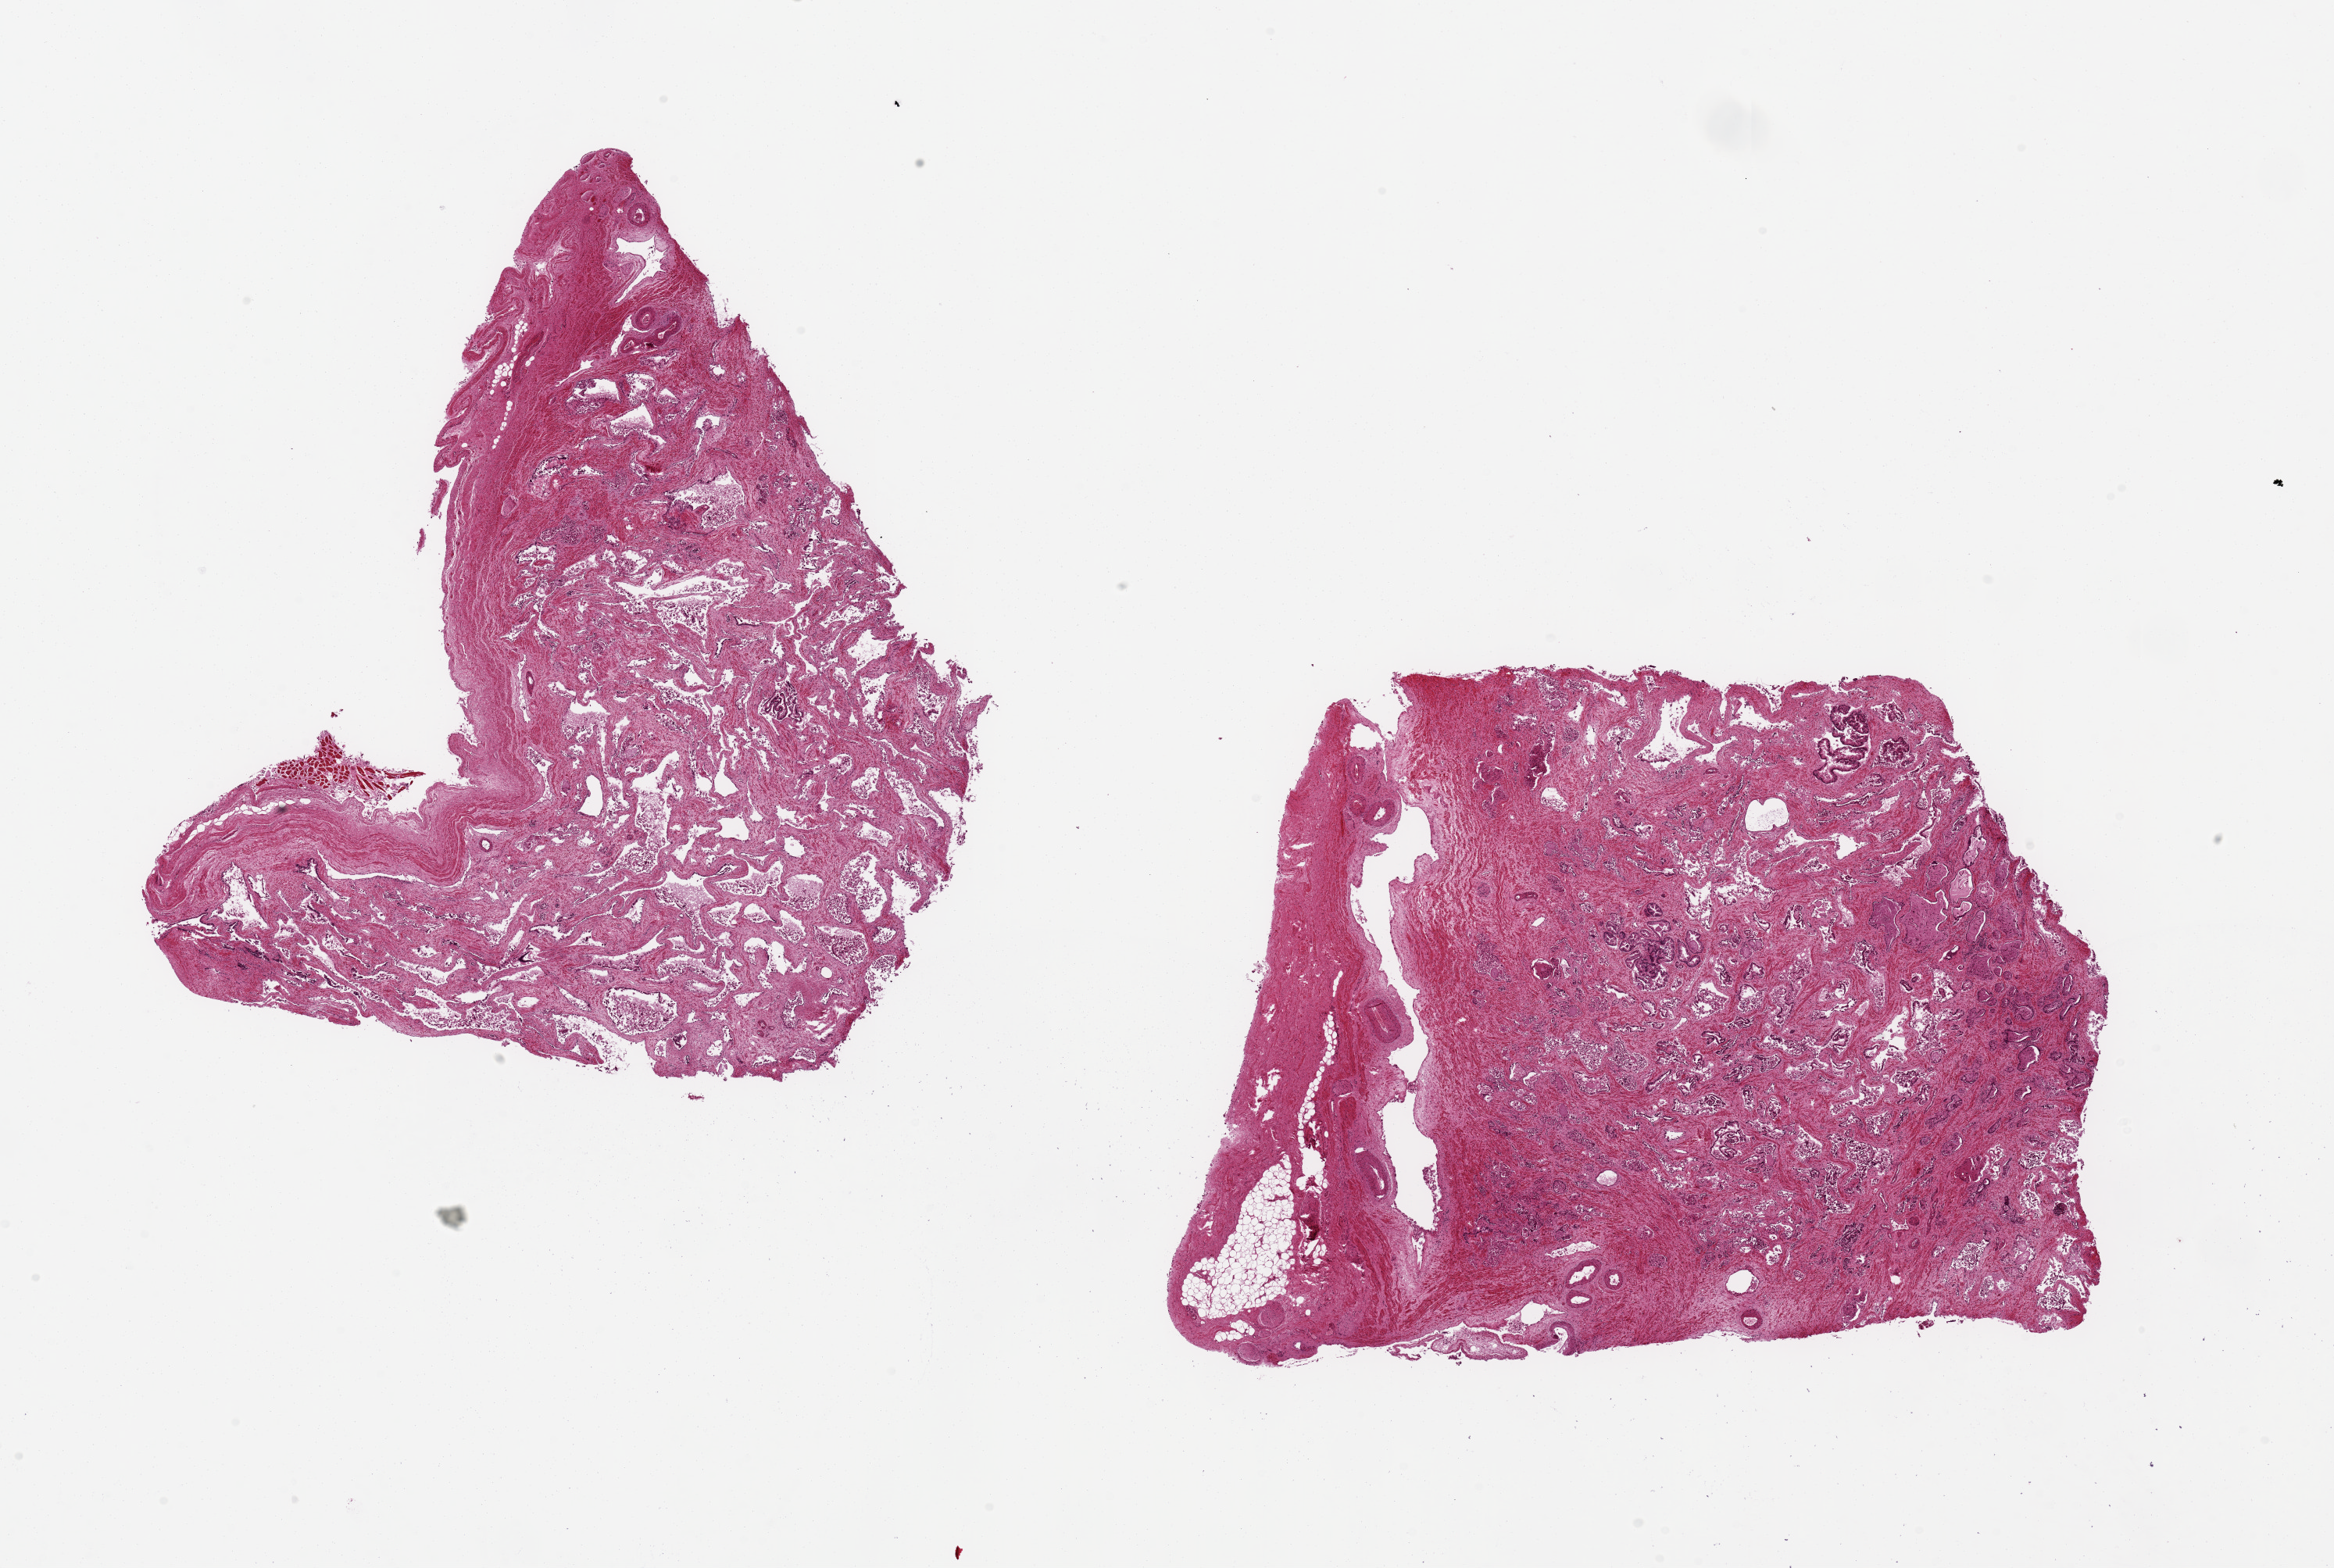
Hematoxylin and eosin (H&E) whole-slide image, whole scanned area (about 23.6 x 15.9 mm) shown as a low-resolution overview; PAXgene-fixed, paraffin-embedded tissue; target tissue: prostate; tissue donor sample.
Review note (as recorded): 2 pieces ~8x7mm. Pattern of glandular hyperplasia but mucosa severely autolyzed.